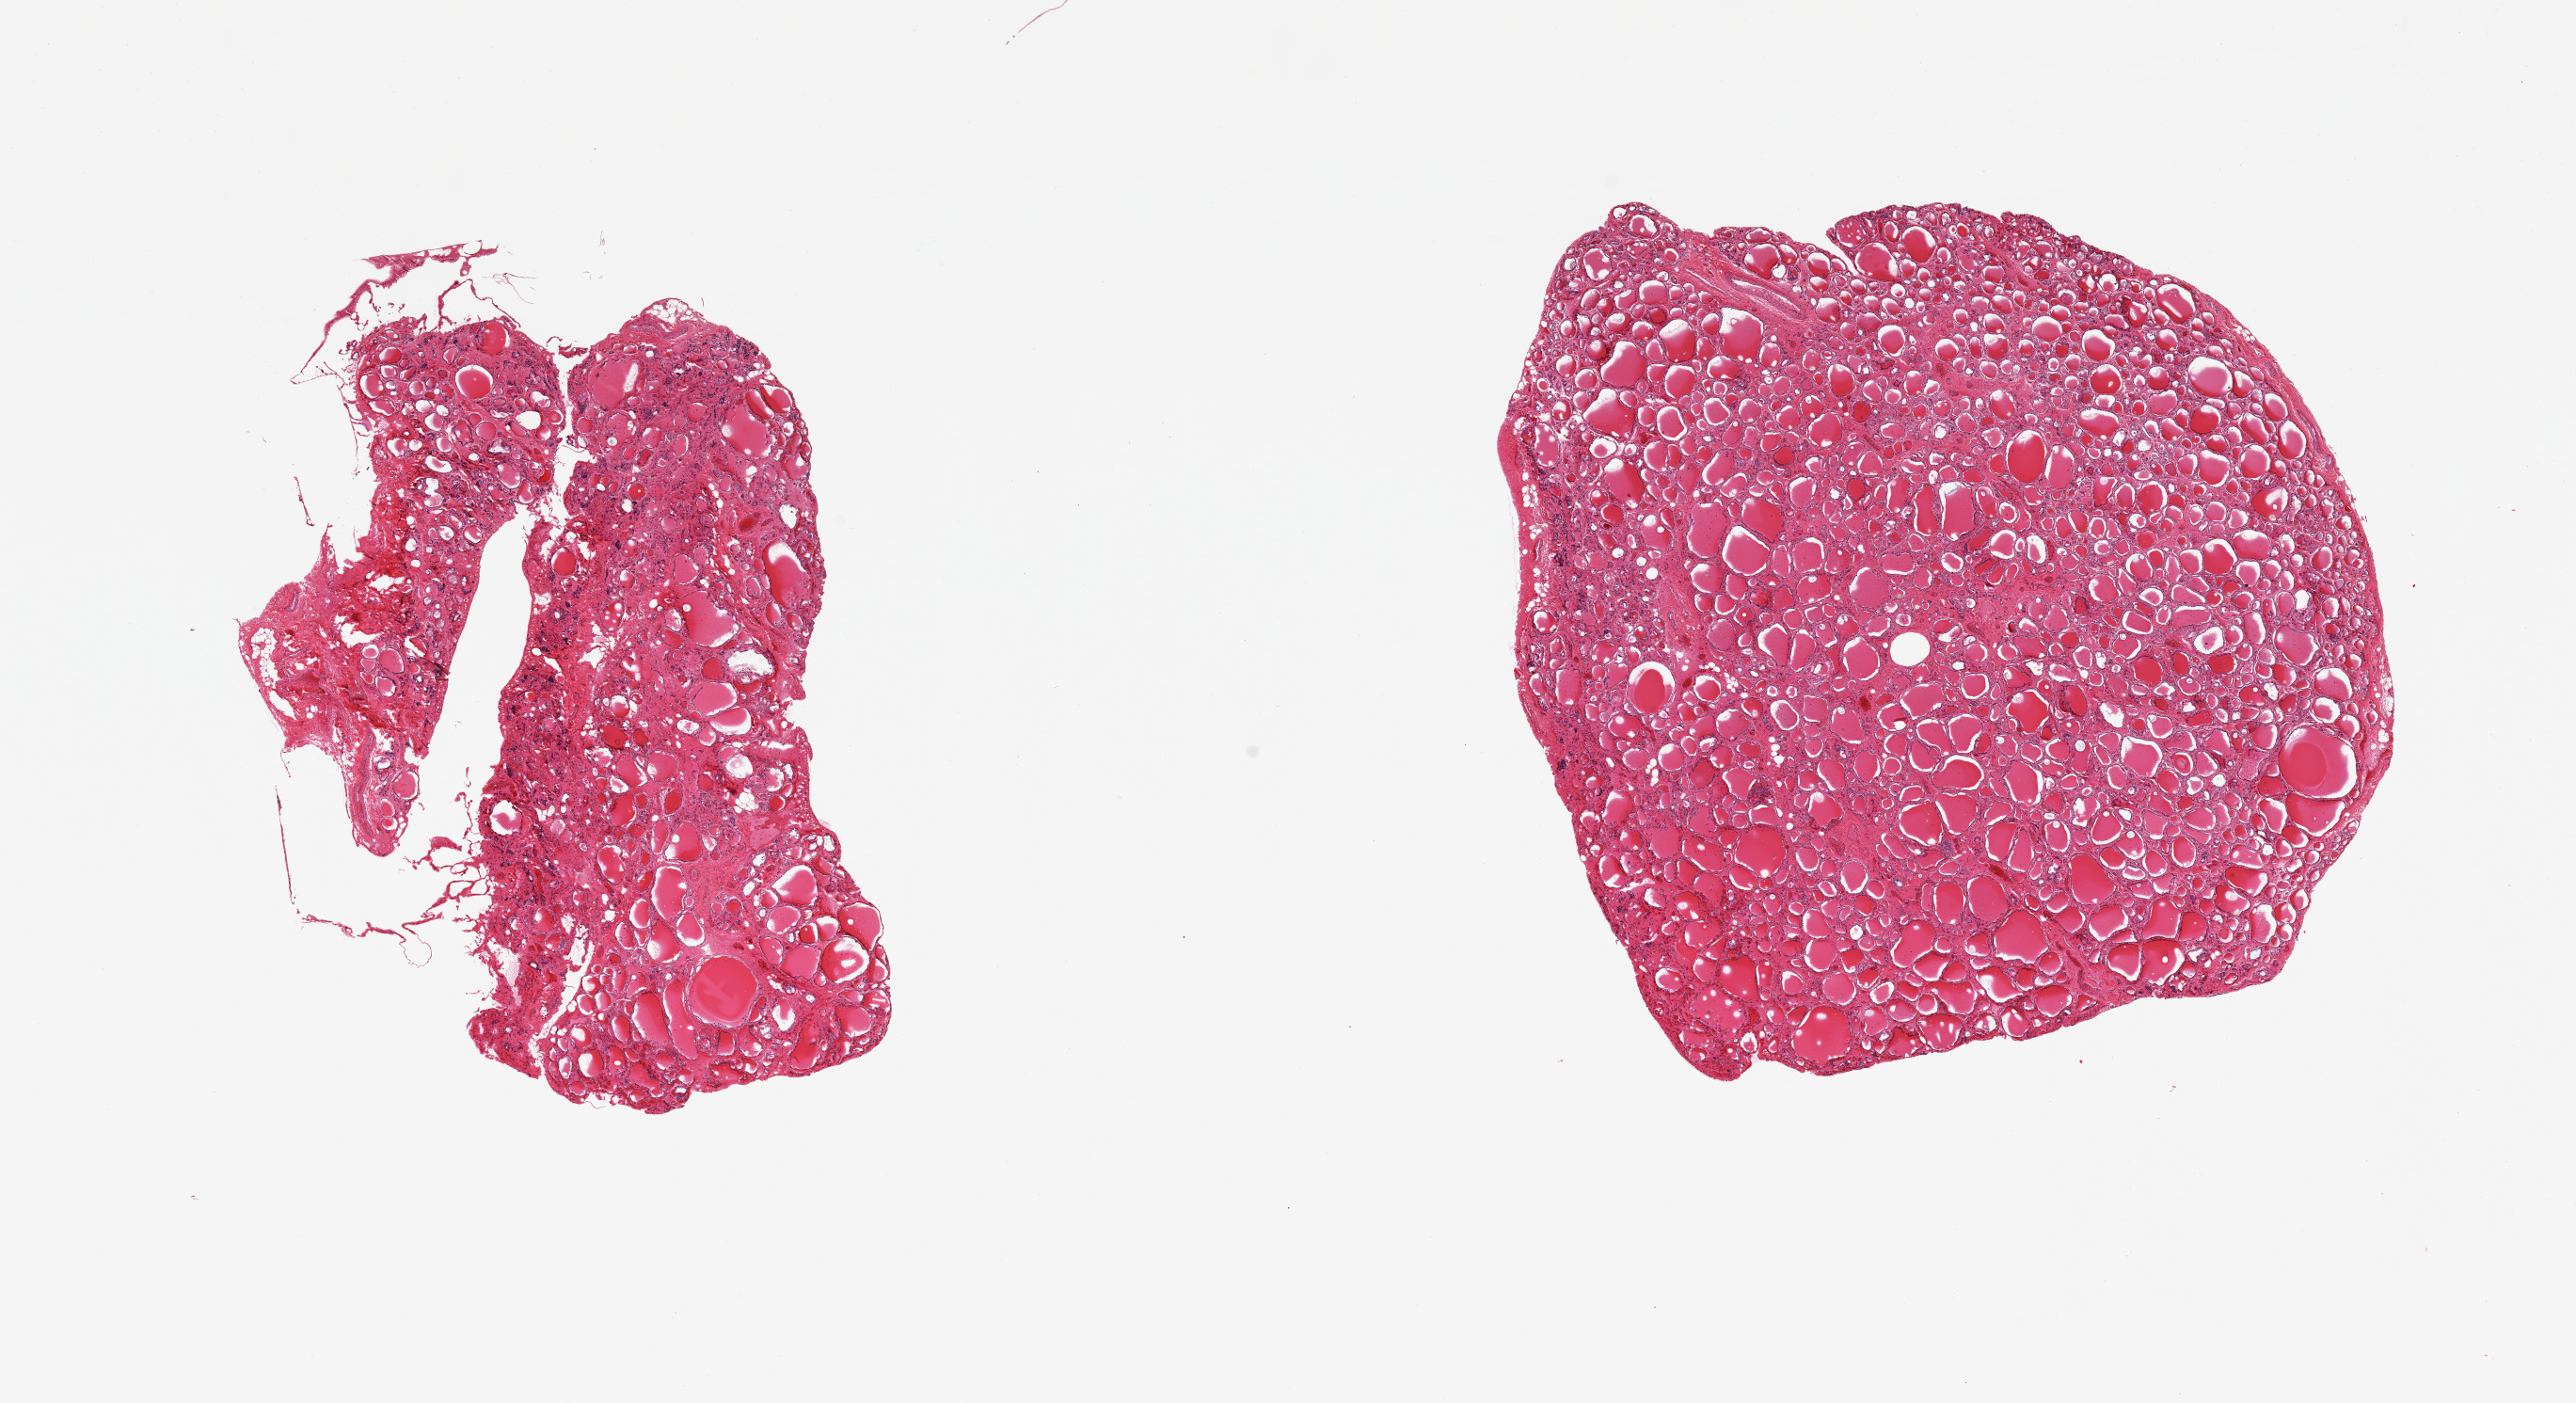
Whole-slide image, haematoxylin and eosin stain, brightfield, shown as a low-resolution overview of the whole scanned area (about 21.7 x 11.8 mm, slide scanned at 20x); PAXgene-fixed, paraffin-embedded tissue; section of thyroid (target tissue); tissue donor sample. Male donor.
Review note (as recorded): 2 pieces.